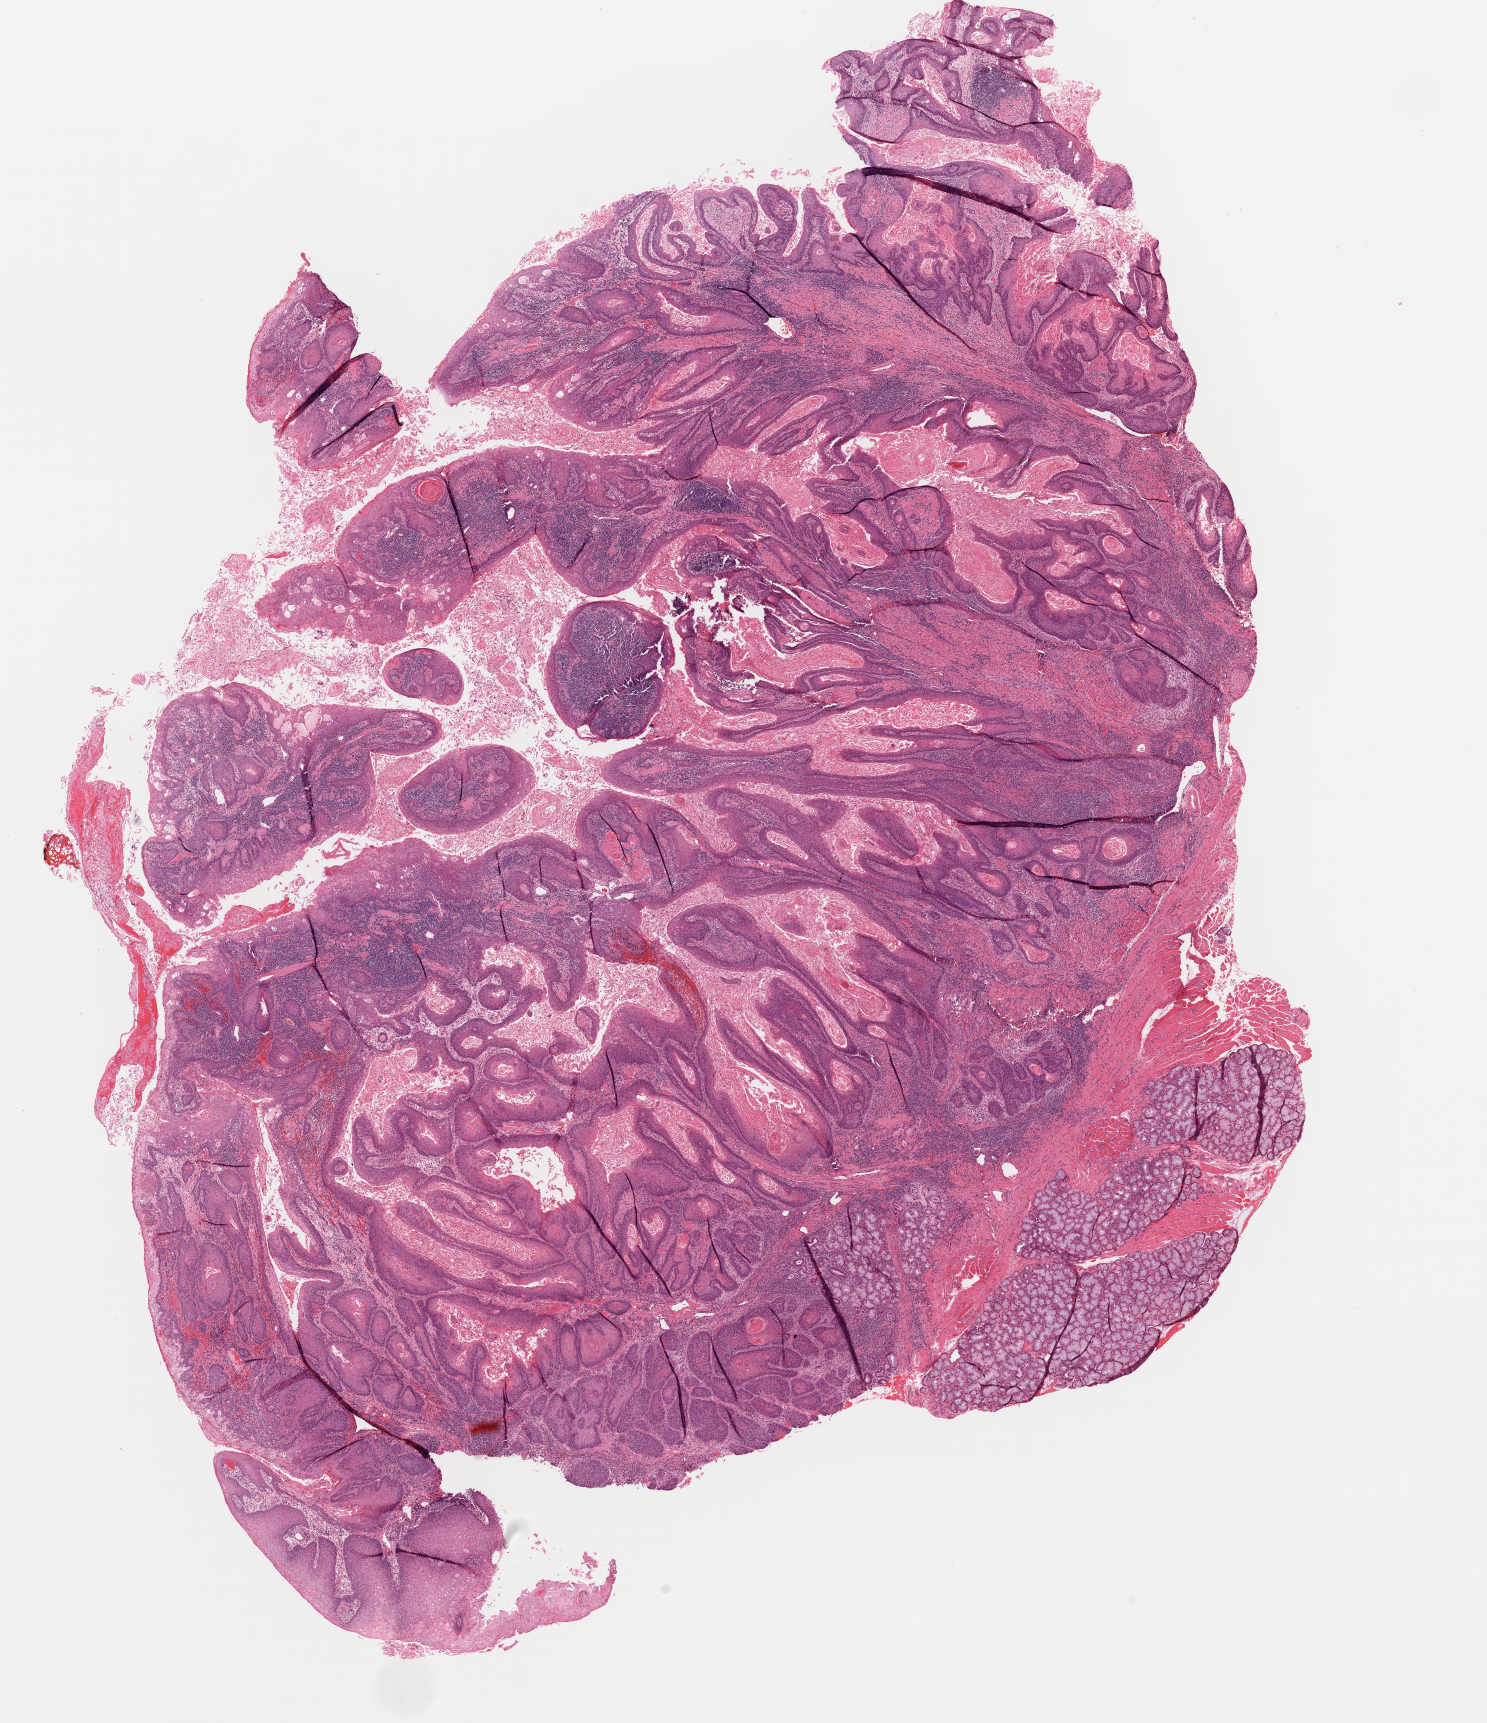
Digitized Hematoxylin and eosin (H&E) stained tissue section (whole slide) — low-resolution overview of the scanned area, about 11.7 x 13.6 mm; FFPE section; head and neck, primary tumour sample. Male, age 54 years at initial diagnosis. Histologic grade: G1 (well differentiated).
• histologic diagnosis: Squamous cell carcinoma, NOS (base of tongue, NOS)
• laterality: left
• AJCC pathologic stage: II (7th edition)
• TNM: T2 N0 M0